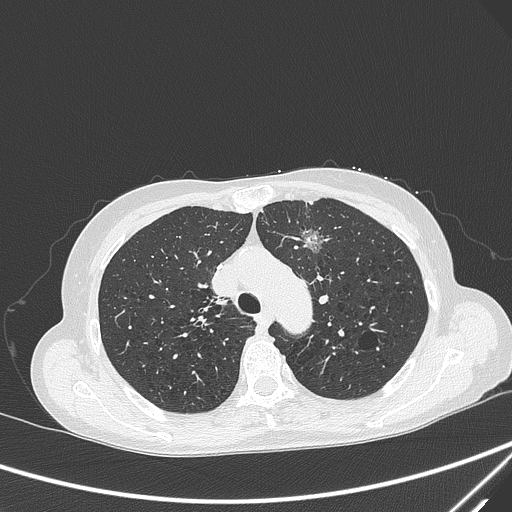
Chest CT, one axial slice; position 220 of 299 along the scan axis; lung window (W 1500 / L -600 HU); 1 mm slice thickness; 512 × 512 image matrix, field of view 350 × 350 mm. Female patient, age 71 years. Case-level facts recorded for this patient, not image findings: clinical TNM (as recorded): T1c N0 M0; histopathological grade: G2-3.
Outlined on this slice (rectangle marked by the reading radiologist):
- lung tumour (recorded histology: adenocarcinoma): box from (x=296, y=224) to (x=331, y=262) px